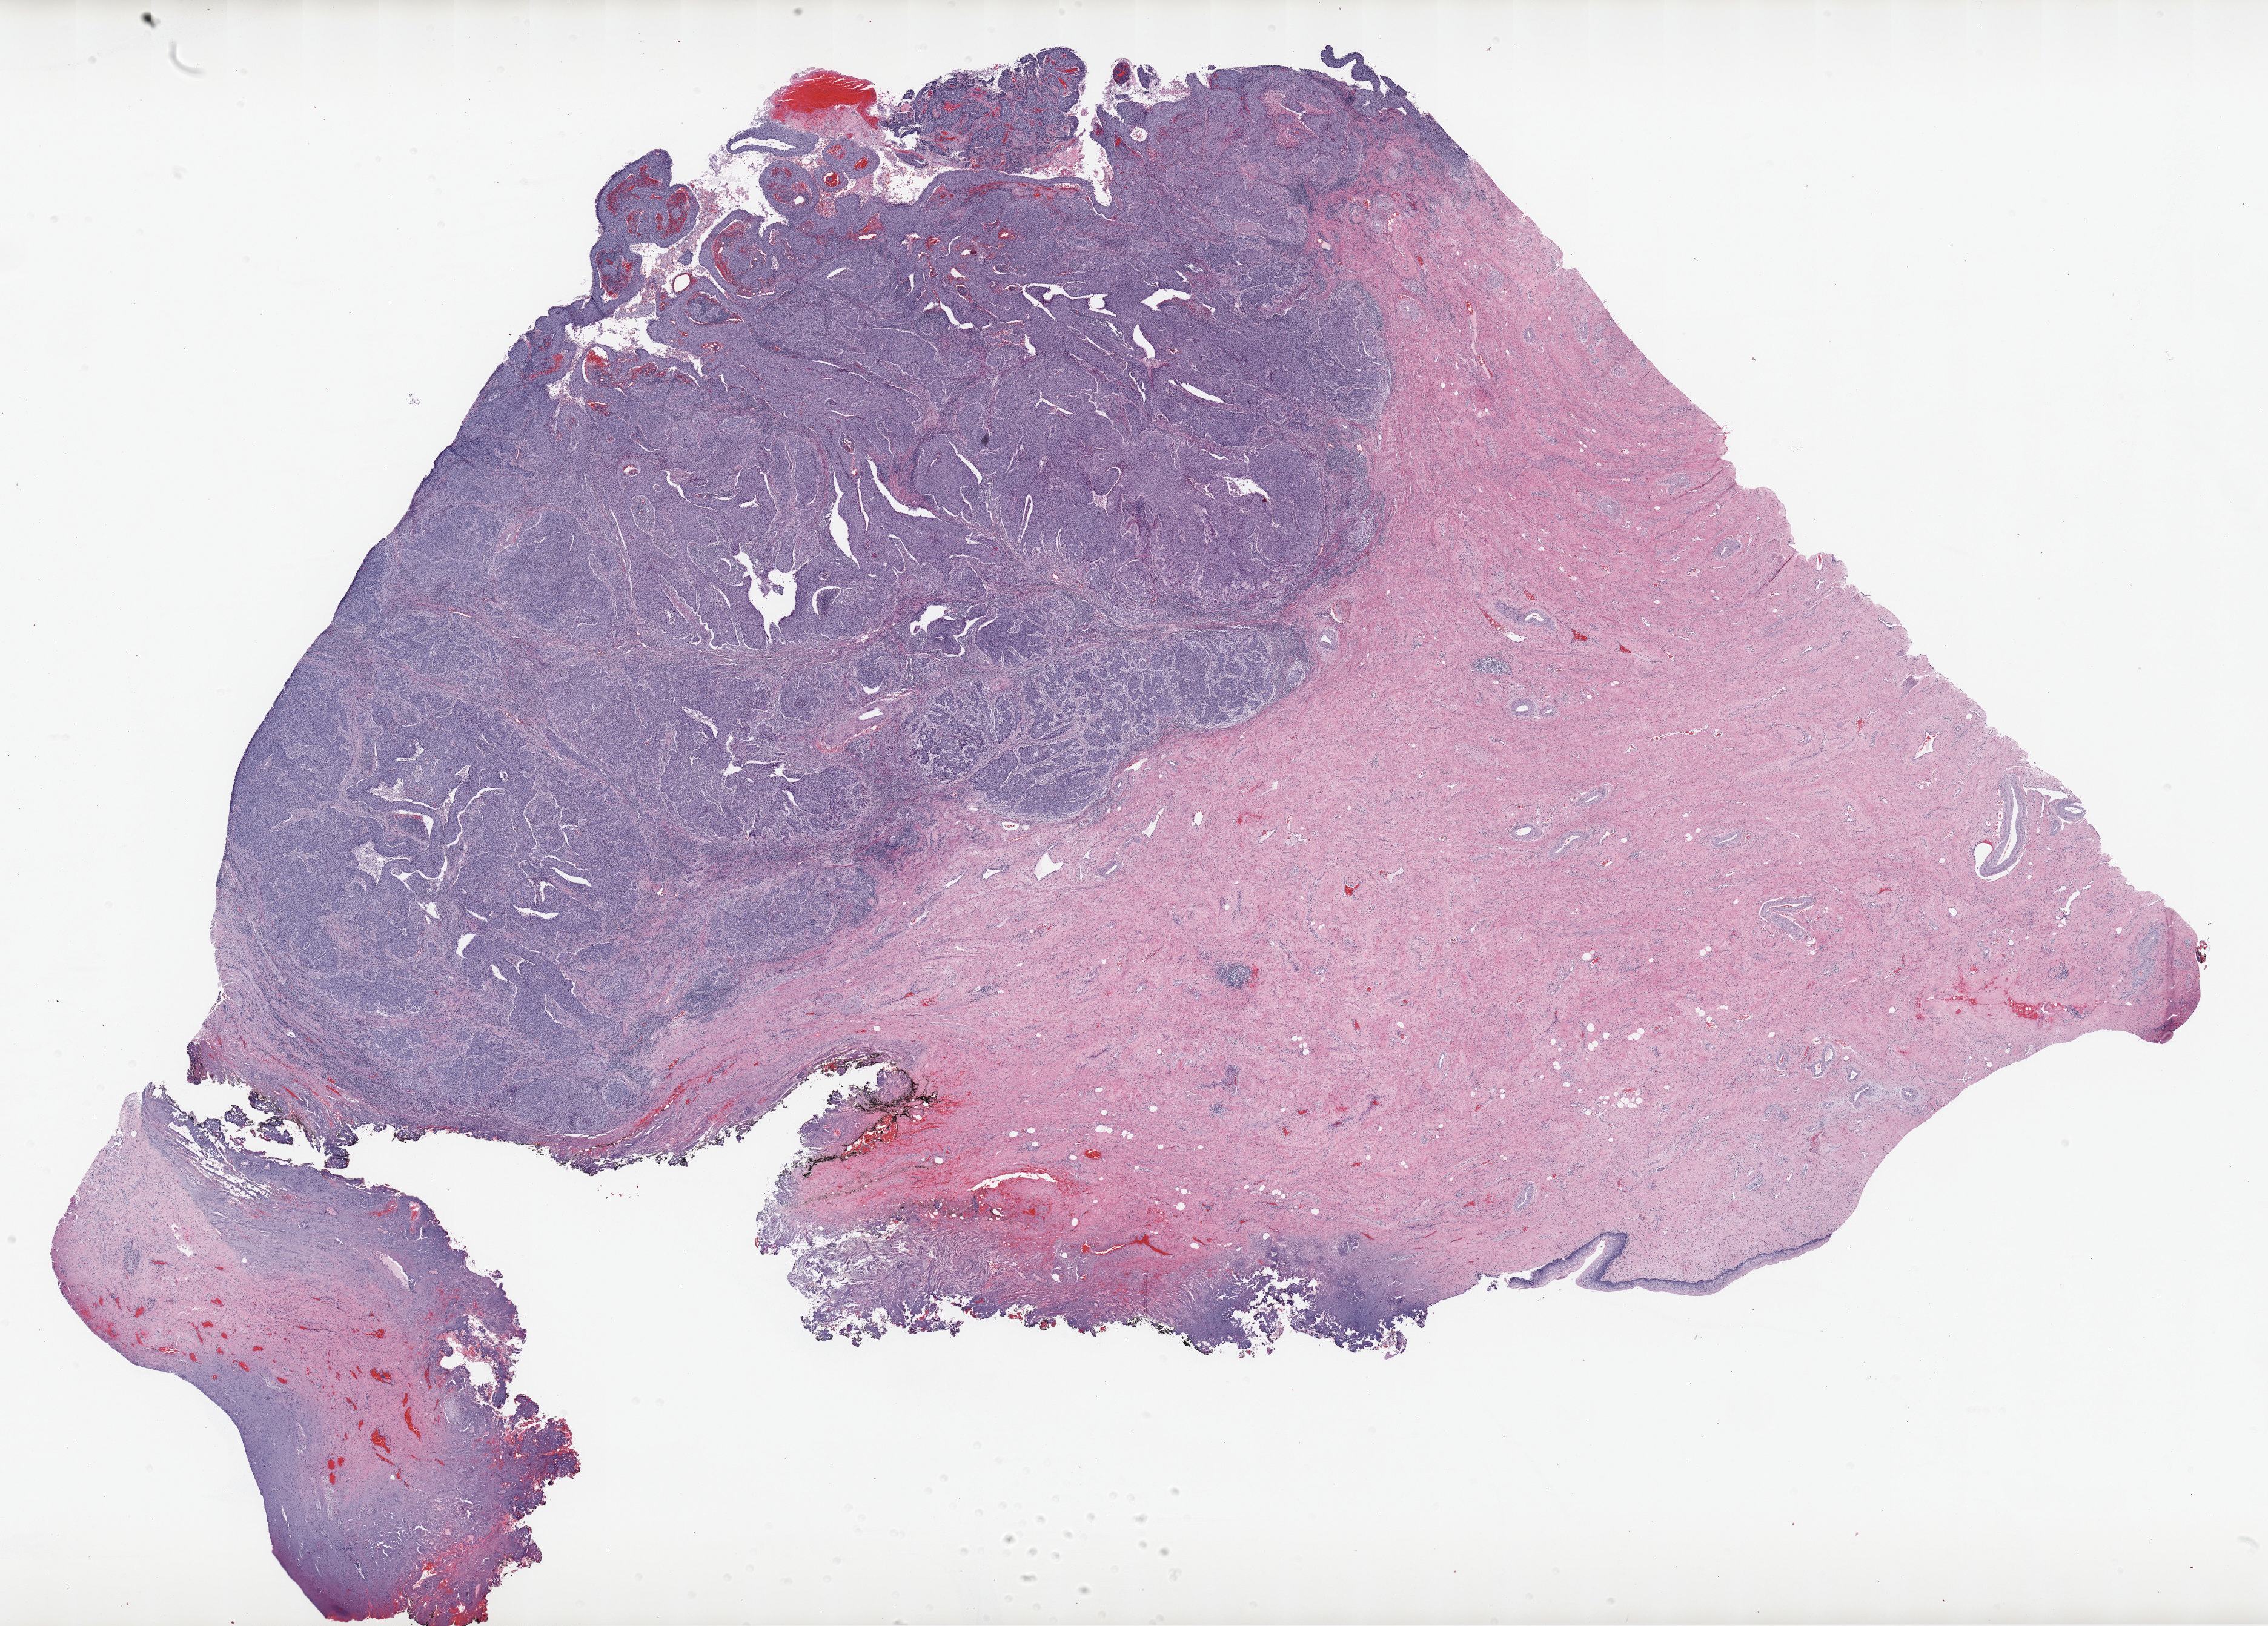
Whole-slide histology image, Hematoxylin and eosin (H&E) stained — shown as a low-resolution overview of the whole scanned area (about 29.8 x 21.4 mm), formalin-fixed paraffin-embedded (FFPE) diagnostic section, primary tumour sample from the cervix. Patient: female, age at initial diagnosis 69 years. Histologic grade: G3 (poorly differentiated).
FIGO stage: IB2. Lymph nodes positive (case pathology): 0 of 17 examined. Diagnosis: Squamous cell carcinoma, NOS (cervix uteri).